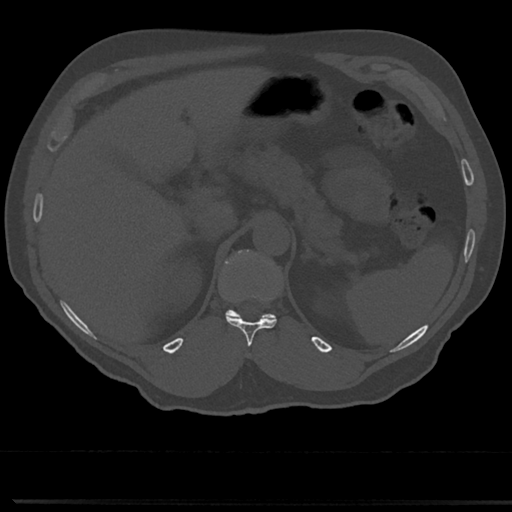
CT including the spine, one axial slice. Slice 181 of 817 in the series (ordered by position). 120 kVp. Bone window (W 1800 / L 400 HU). 0.5 mm slice thickness. 512 × 512 image matrix, field of view 355 × 355 mm. Patient: male, 61 years. From the clinical record (not read from this slice): primary cancer: prostate.
Outlined on this slice (semi-automatic segmentation, software-assisted and operator-edited):
- T11 vertebra: bounding box (x1, y1, x2, y2) in pixels: (226, 317, 277, 349)
- T12 vertebra: (221, 250, 276, 321)